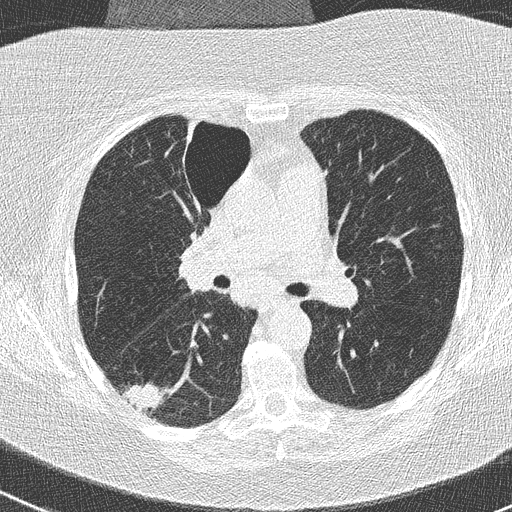
Low-dose screening chest CT, one axial slice; position 155 of 261 along the scan axis; lung window (W 1500 / L -600 HU); 2 mm slice thickness; 512 × 512 image matrix, field of view 310 × 310 mm.
Structures marked on this image (expert manual segmentation):
- lesion 1 (tumor, lower lobe of right lung): box from (x=125, y=383) to (x=164, y=413) px